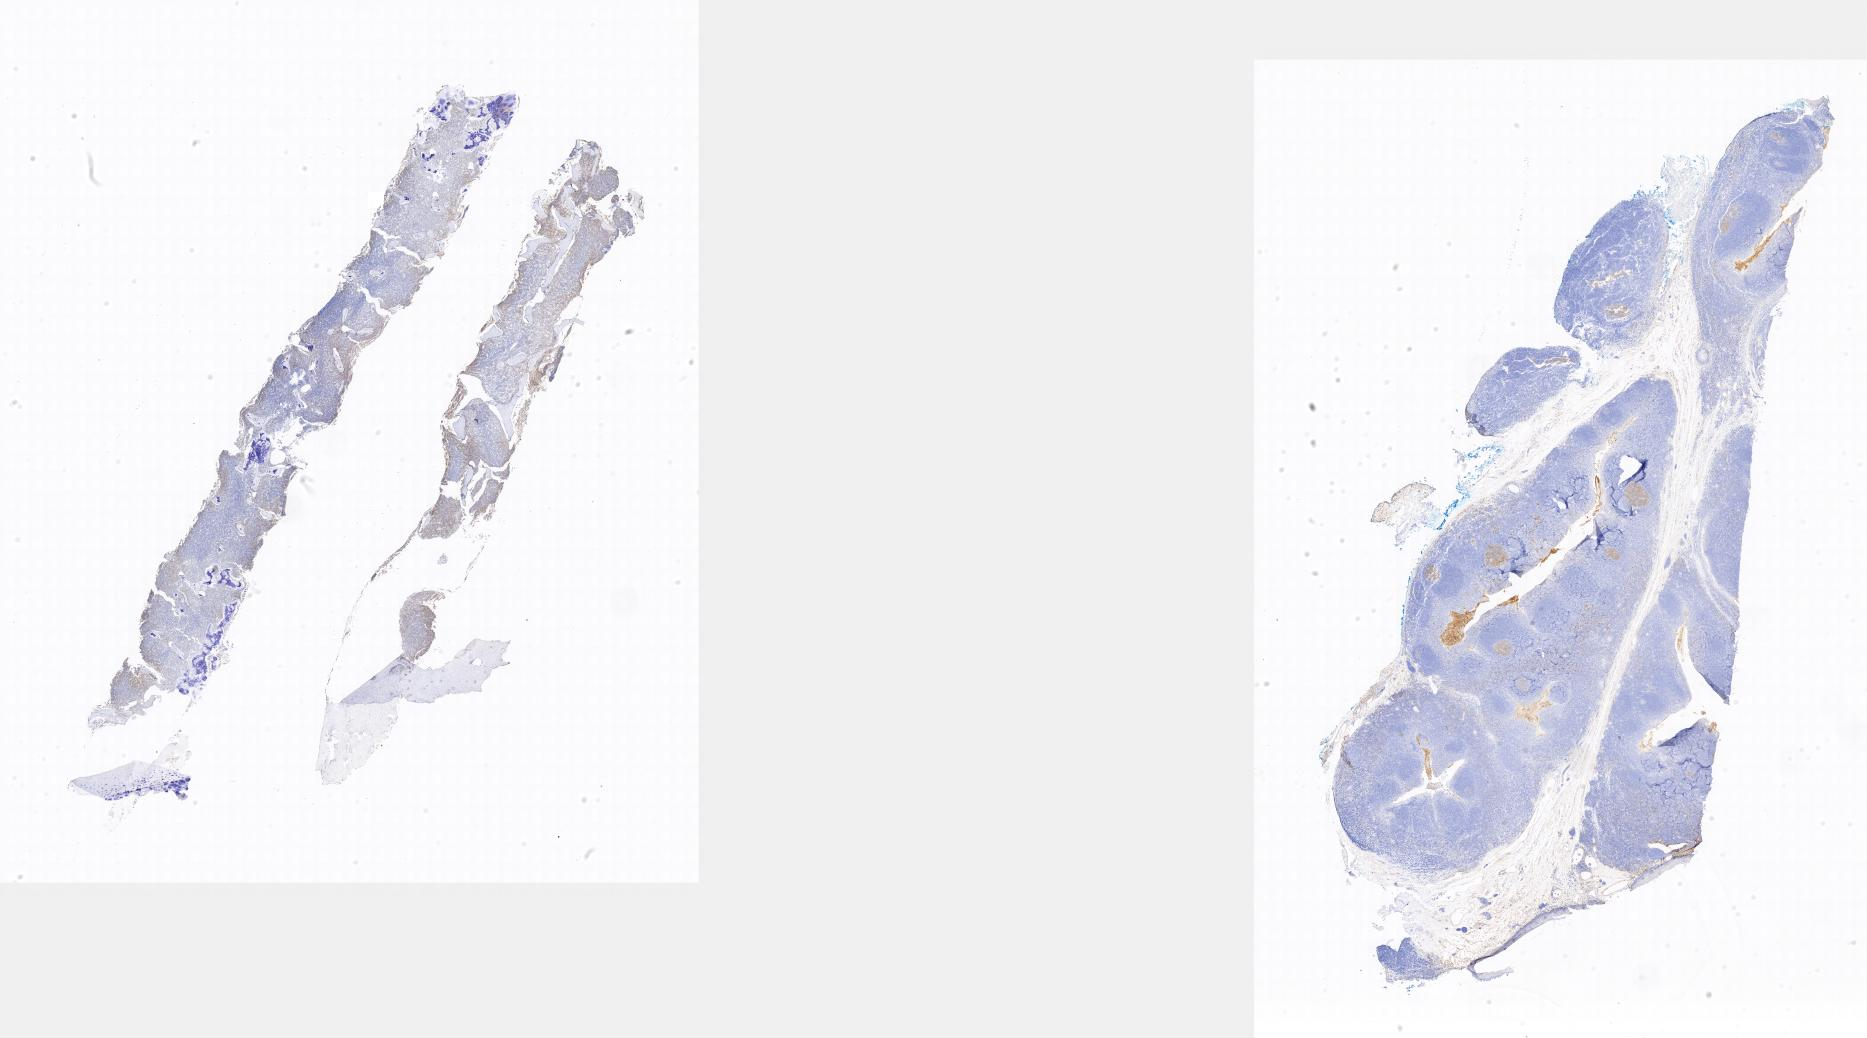
Whole-slide image, immunohistochemical stain for CD10, a low-resolution overview of the entire scanned area; tumor tissue; anatomic site: bone marrow. Male patient, 16 years old.
Diagnosis: Burkitt lymphoma, NOS.